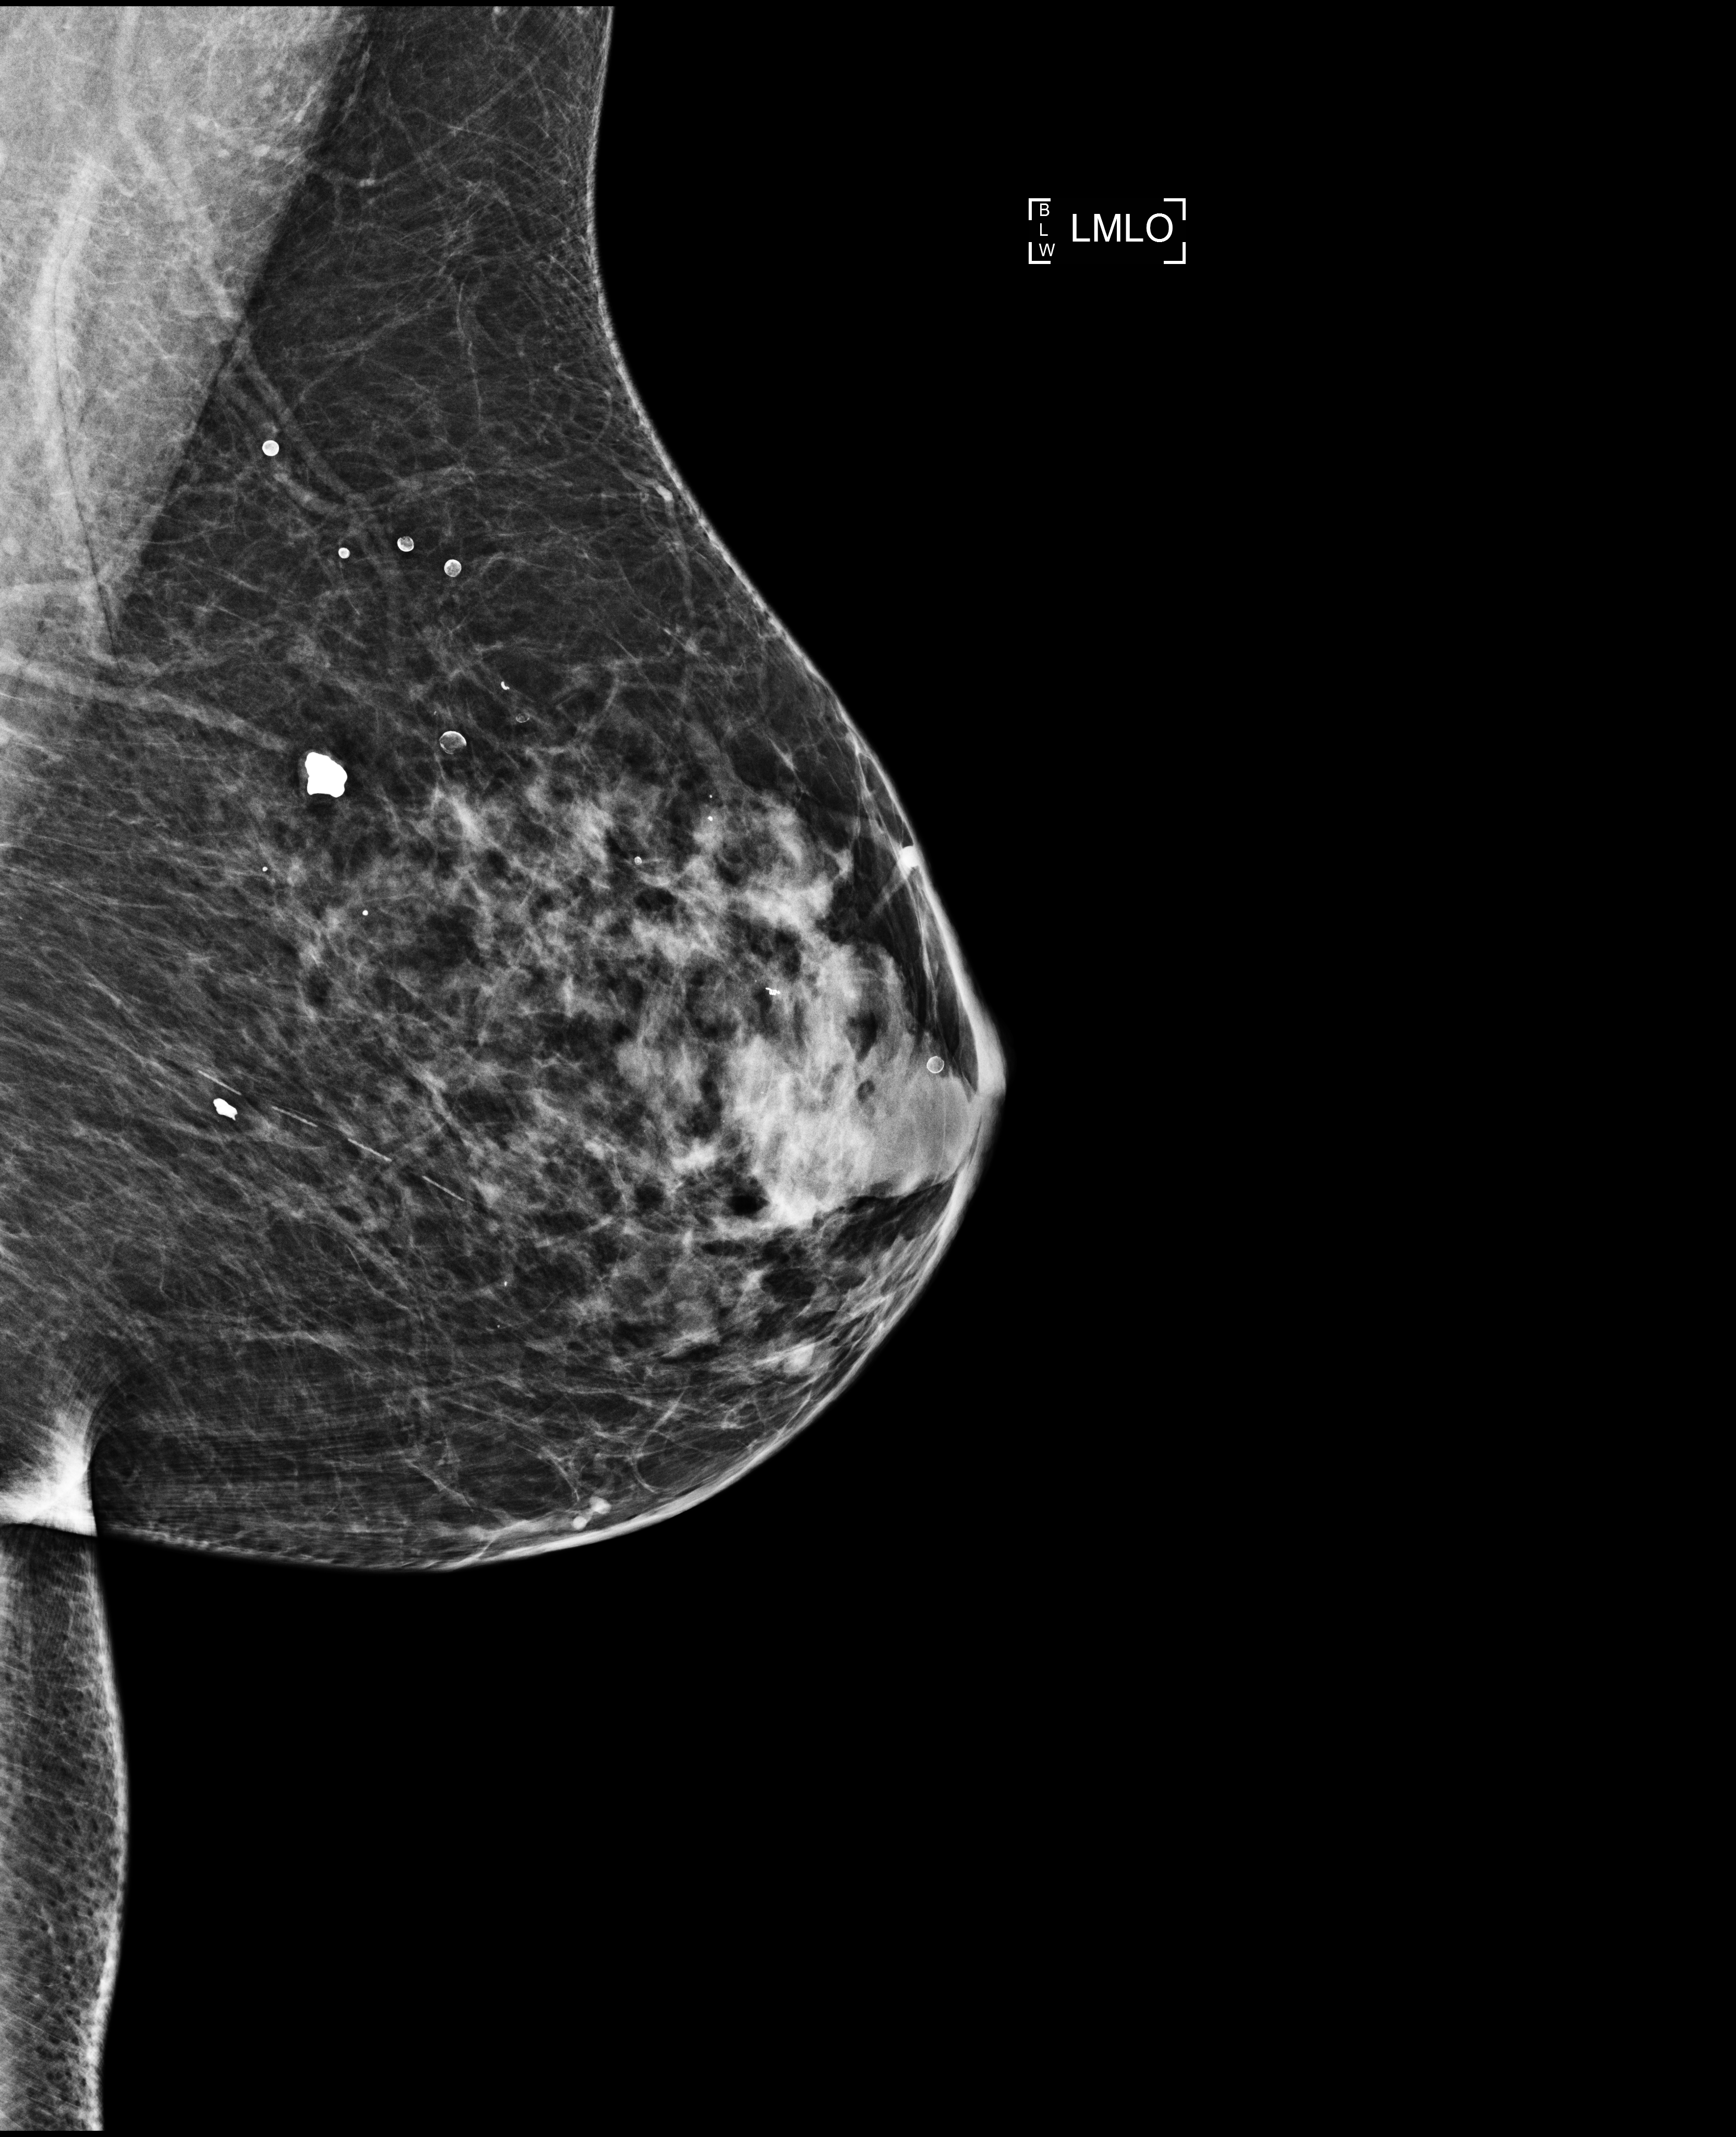
Annual screening mammography examination, compressed breast thickness 44 mm. Female patient, age 69 years.
Image type: full-field digital mammogram. Breast: left. Projection: mediolateral oblique (MLO) view.